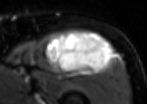
MRI of an extremity soft-tissue mass, one axial slice; position 66 of 85 along the scan axis; T2-weighted fat-saturated; MR volume resampled by the dataset authors to the PET/CT grid (not the native acquisition matrix); 3.27 mm slice thickness; 147 × 104 image matrix, field of view 144 × 102 mm. Male patient. Case-level facts recorded for this patient, not image findings: histological type: extraskeletal osteosarcoma; grade: high; site of the primary tumour: thigh.
Structures marked on this image (expert contour drawn on MRI and transferred to this co-registered scan by the dataset authors):
- gross tumour volume (mass): bounding box <44,31,114,73> (left, top, right, bottom; pixels)